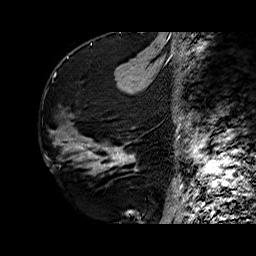
Breast MRI (dynamic contrast-enhanced), one sagittal slice. Slice 24 of 60 in the series (ordered by position). Dynamic contrast-enhanced series, time point 2 of 6 at this slice position (early post-contrast). 1.5 T. TE 6.4 ms, TR 32.7 ms. 4 mm slice thickness. 256 × 256 image matrix. Female patient. Case-level facts recorded for this patient, not image findings: setting: breast cancer imaged before/during neoadjuvant chemotherapy; receptor status: HR-positive, HER2-negative.
Annotated regions visible in this slice (semi-automatic segmentation, software-assisted and operator-edited):
- analysis volume of interest (the breast-tissue region the enhancement analysis was run in; not a lesion): bounding box (x1, y1, x2, y2) in pixels: (73, 116, 139, 174)
- tumour enhancement mask (voxels above the 100 % enhancement threshold inside the analysis volume of interest): (112, 148, 125, 164)